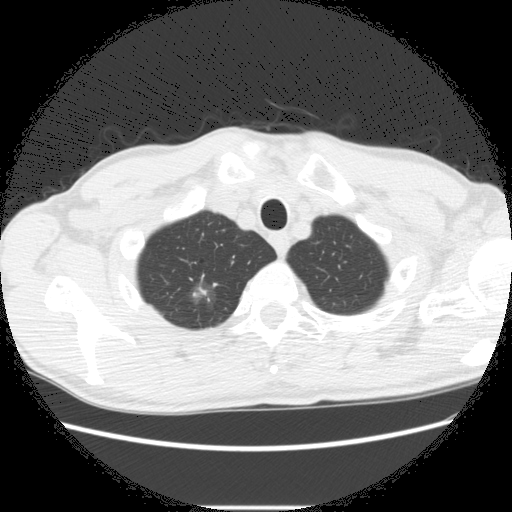
Low-dose screening chest CT, one axial slice; slice 255 of 282 in the series (ordered by position); reconstruction kernel STANDARD; lung window (W 1500 / L -600 HU); 2.5 mm slice thickness; 512 × 512 image matrix, field of view 360 × 360 mm.
Annotated regions visible in this slice (expert manual segmentation):
- lesion 2 (nodule, upper lobe of right lung): bounding box [x1, y1, x2, y2] px = [191, 285, 211, 303]